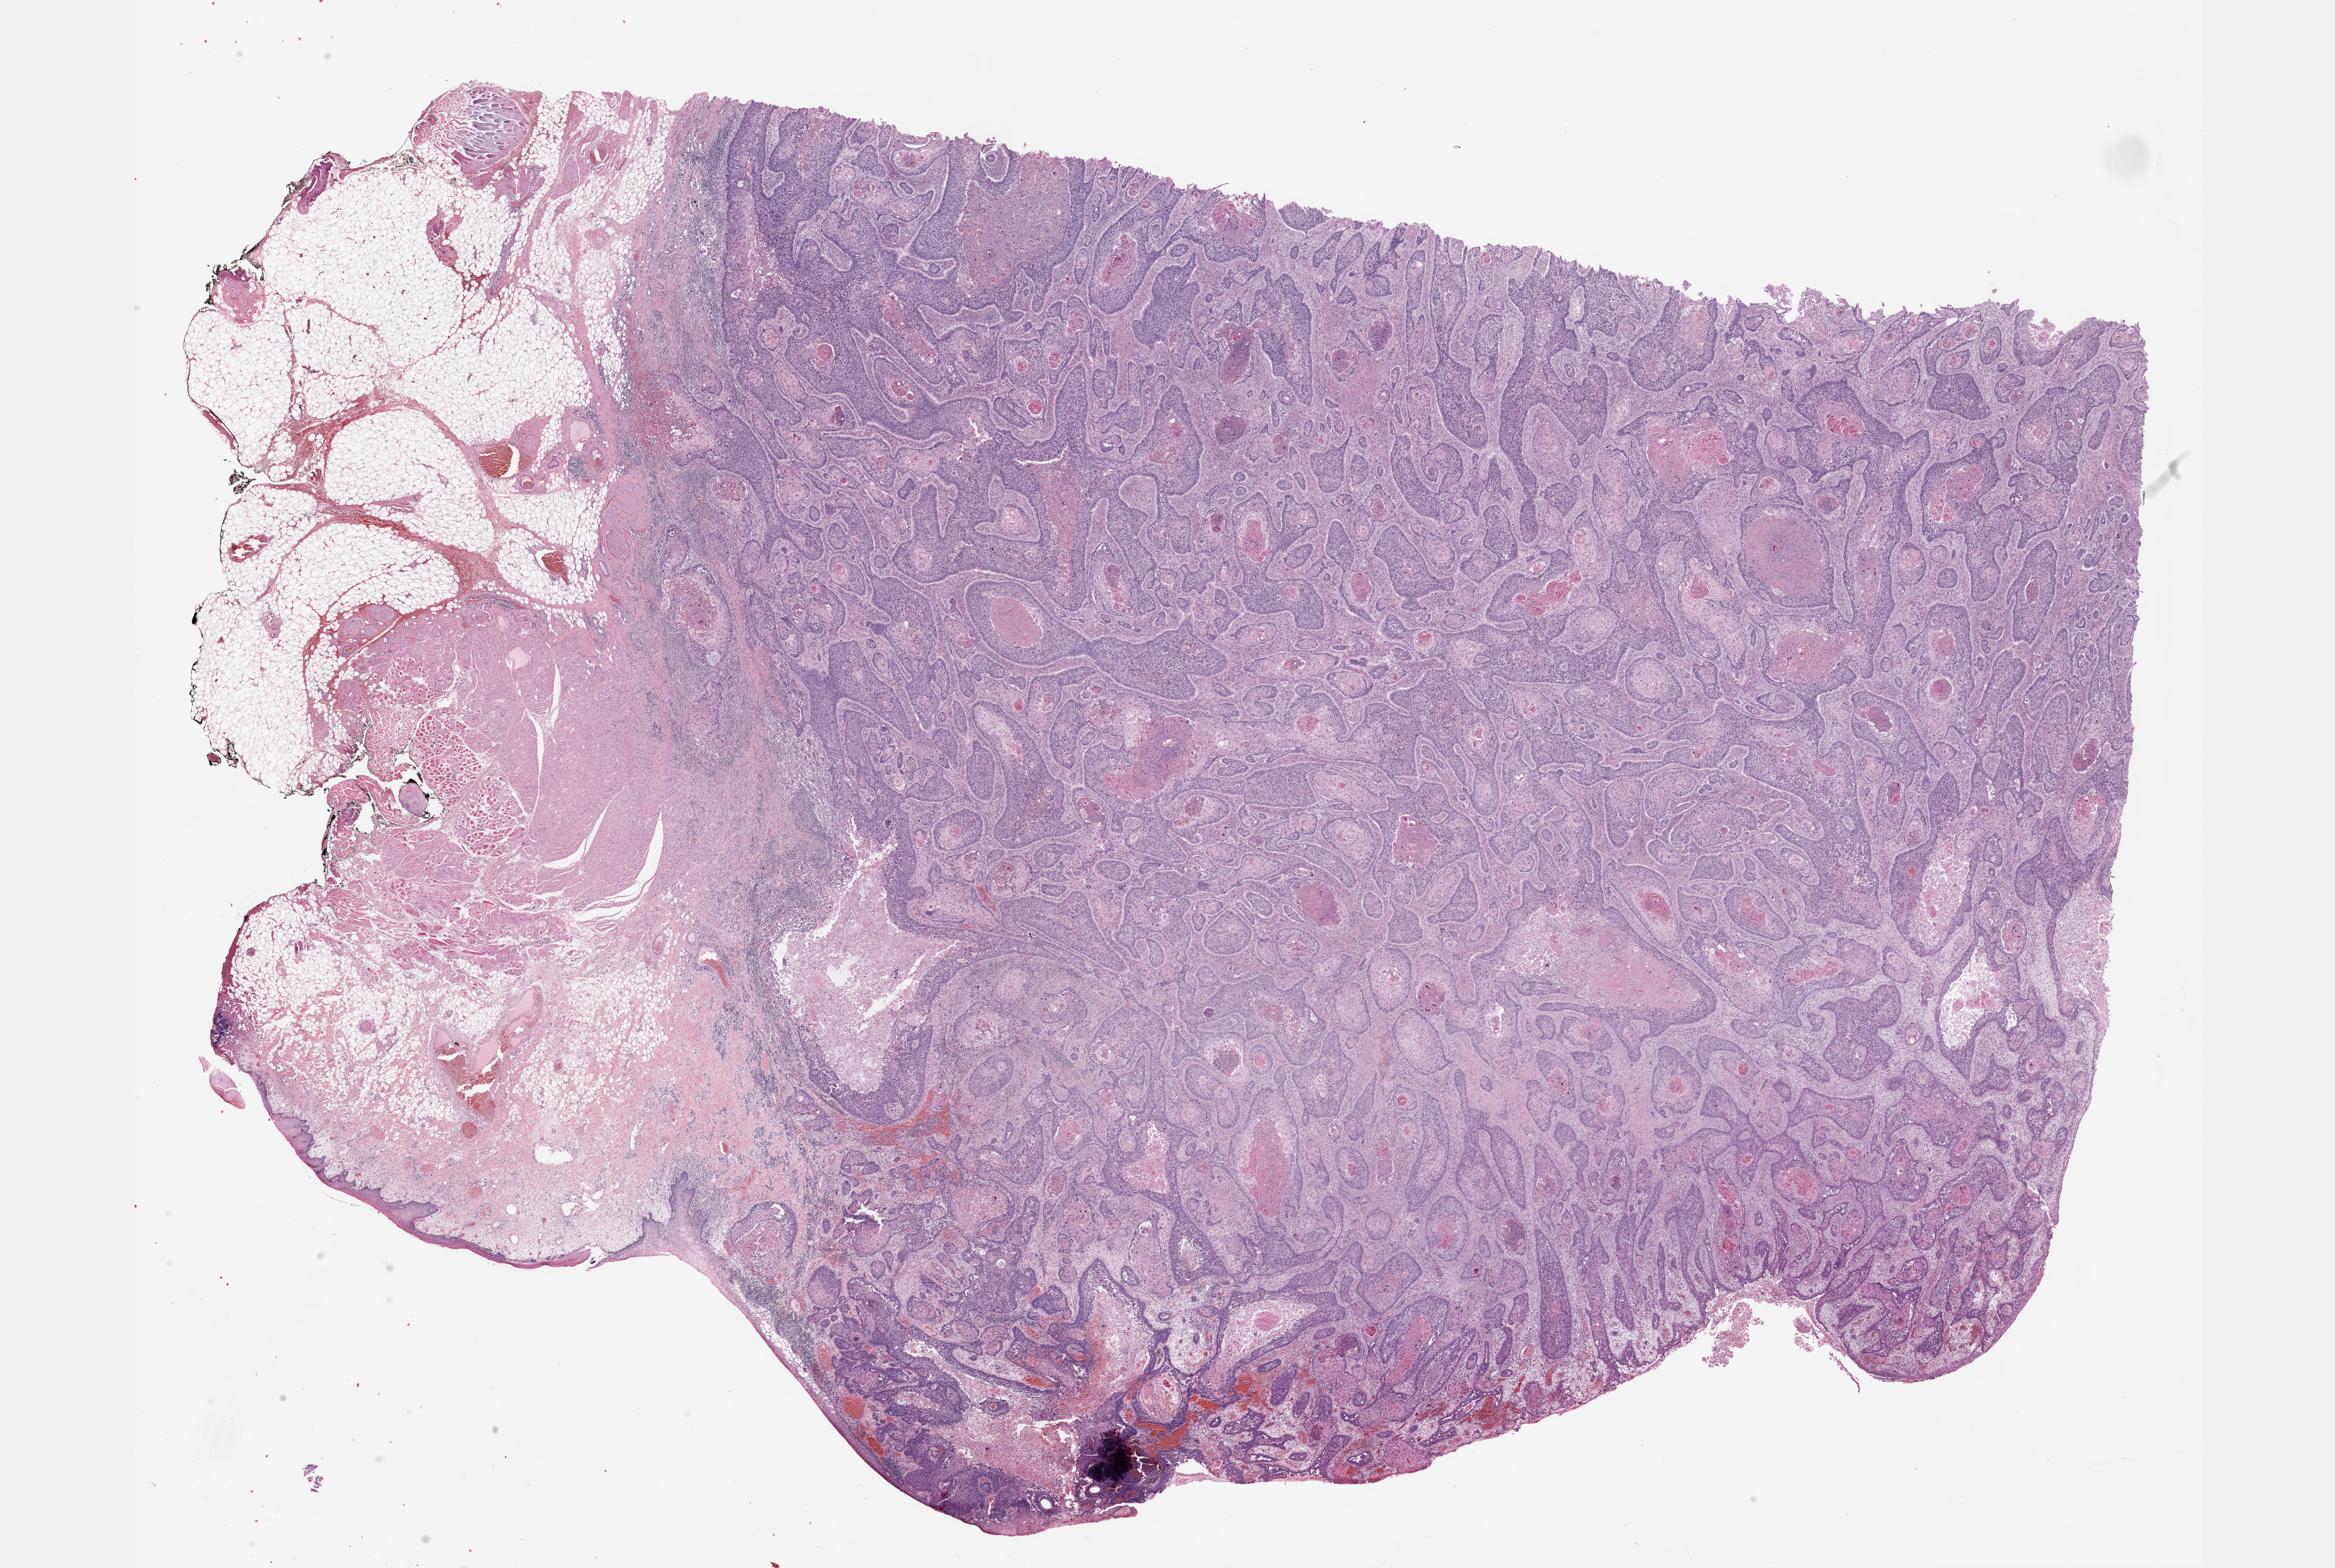
H&E-stained whole-slide image, whole scanned area (about 26.2 x 17.6 mm, slide scanned at 40x) shown as a low-resolution overview, formalin-fixed paraffin-embedded (FFPE) diagnostic section, head and neck, primary tumour sample. Male patient; age at initial diagnosis 50 years. Histologic grade: G2 (moderately differentiated).
AJCC pathologic stage: IVA (7th edition). Lymph nodes positive (case pathology): 0 of 11 examined. Pathologic diagnosis: Squamous cell carcinoma, NOS (gum, NOS). Laterality: right.